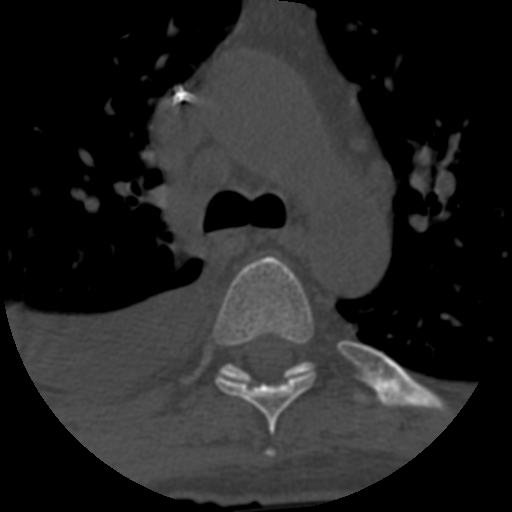
CT including the spine, one axial slice; slice 449 of 708 in the series (ordered by position); 120 kVp; one of 3 acquisitions stored at this slice position; bone window (W 1800 / L 400 HU); 1.25 mm slice thickness; 512 × 512 image matrix, field of view 160 × 160 mm. Patient age 55 years. From the clinical record (not read from this slice): primary cancer: colon; vertebrae with lytic lesions (as recorded): T12, L1, L5.
Structures marked on this image (semi-automatically segmented with operator editing):
- T5 vertebra: box from (x=214, y=256) to (x=315, y=434) px
- T6 vertebra: (x=219, y=361)–(x=366, y=402)